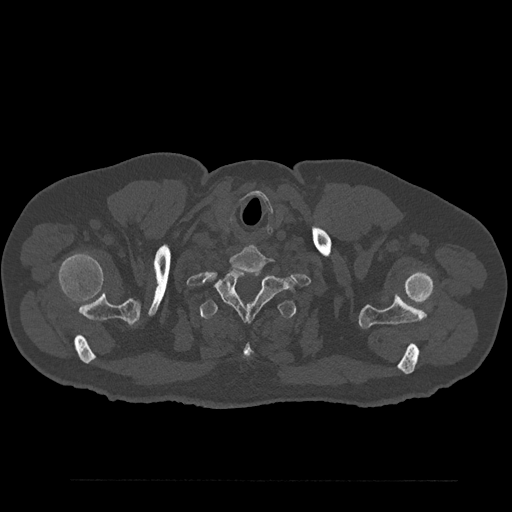
CT including the spine, one axial slice. Slice 749 of 797 in the series (ordered by position). Reconstruction kernel Br40s/3. 120 kVp. Bone window (W 1800 / L 400 HU). 0.5 mm slice thickness. 512 × 512 image matrix, field of view 430 × 430 mm. Male patient, age 61 years. Case-level facts recorded for this patient, not image findings: primary cancer: prostate.
Outlined on this slice (semi-automatically segmented with operator editing):
- T1 vertebra: bounding box [x1, y1, x2, y2] px = [217, 269, 293, 321]
- T2 vertebra: [200, 299, 296, 360]